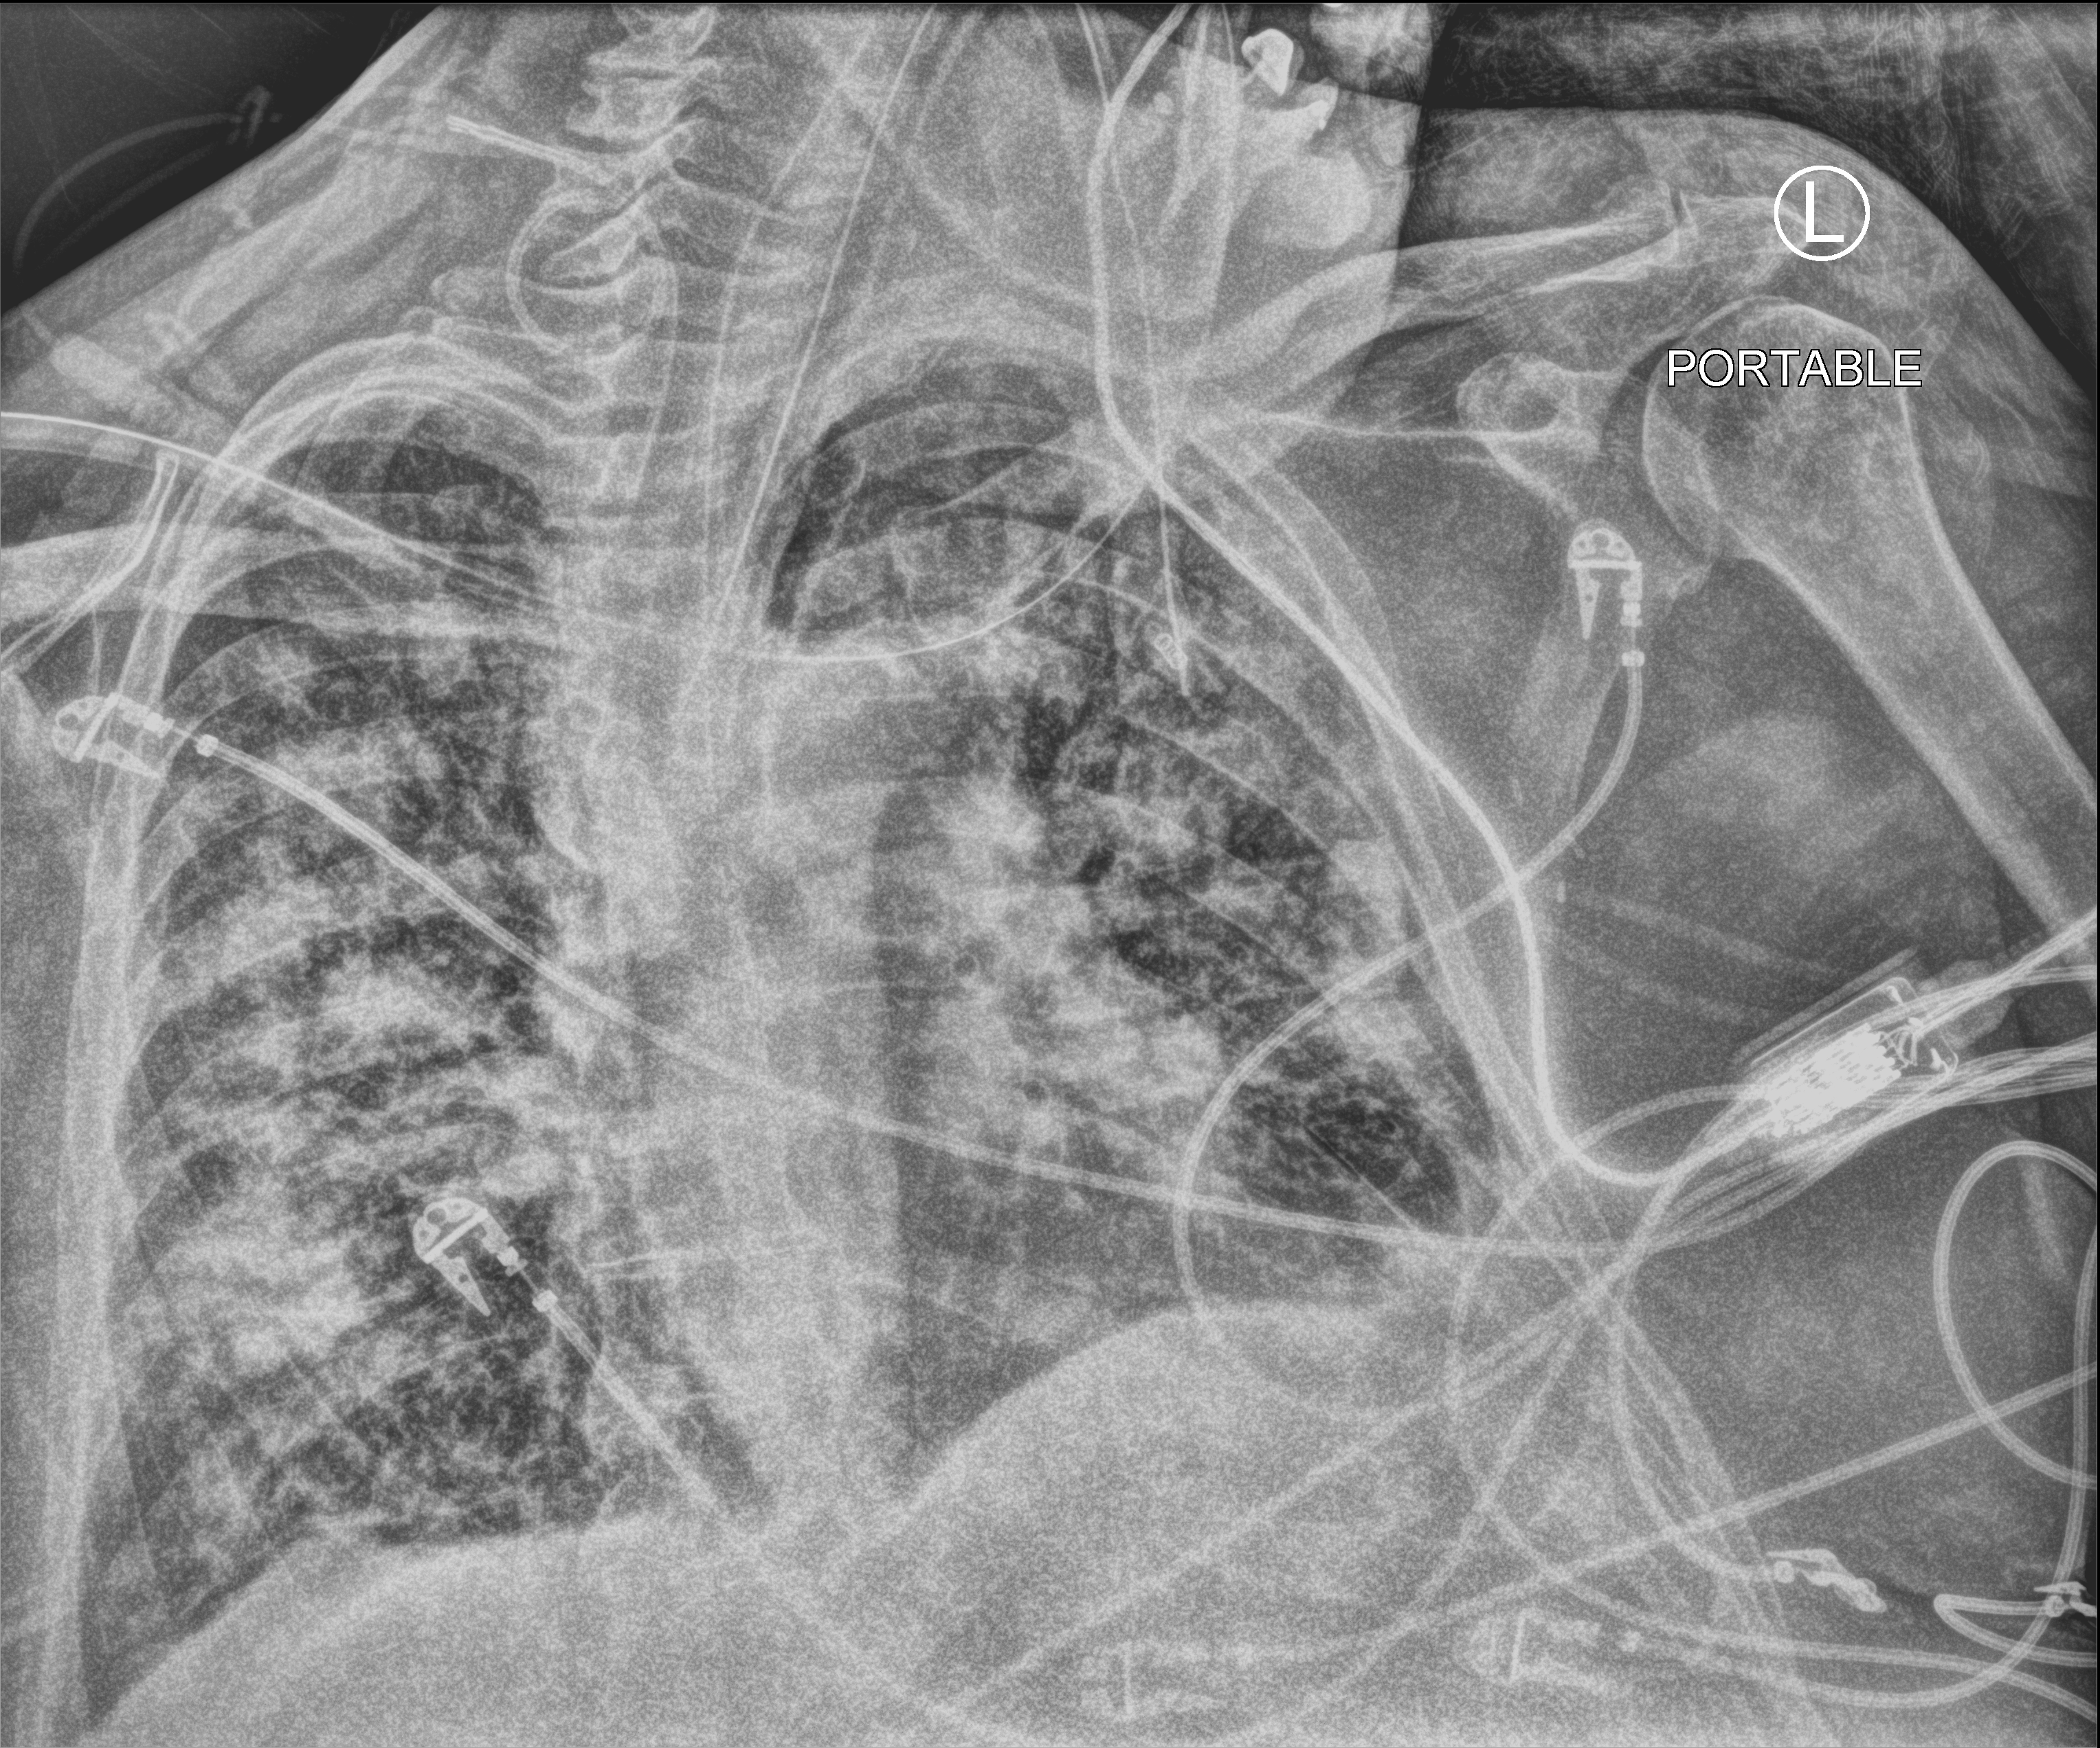
Portable chest radiograph; anteroposterior (AP) projection. Male patient hospitalised with COVID-19, age 60–74 years.
Hospital-stay facts (about this admission, not read from this image; timing relative to this image not recorded): chronic kidney disease (admission record): no.